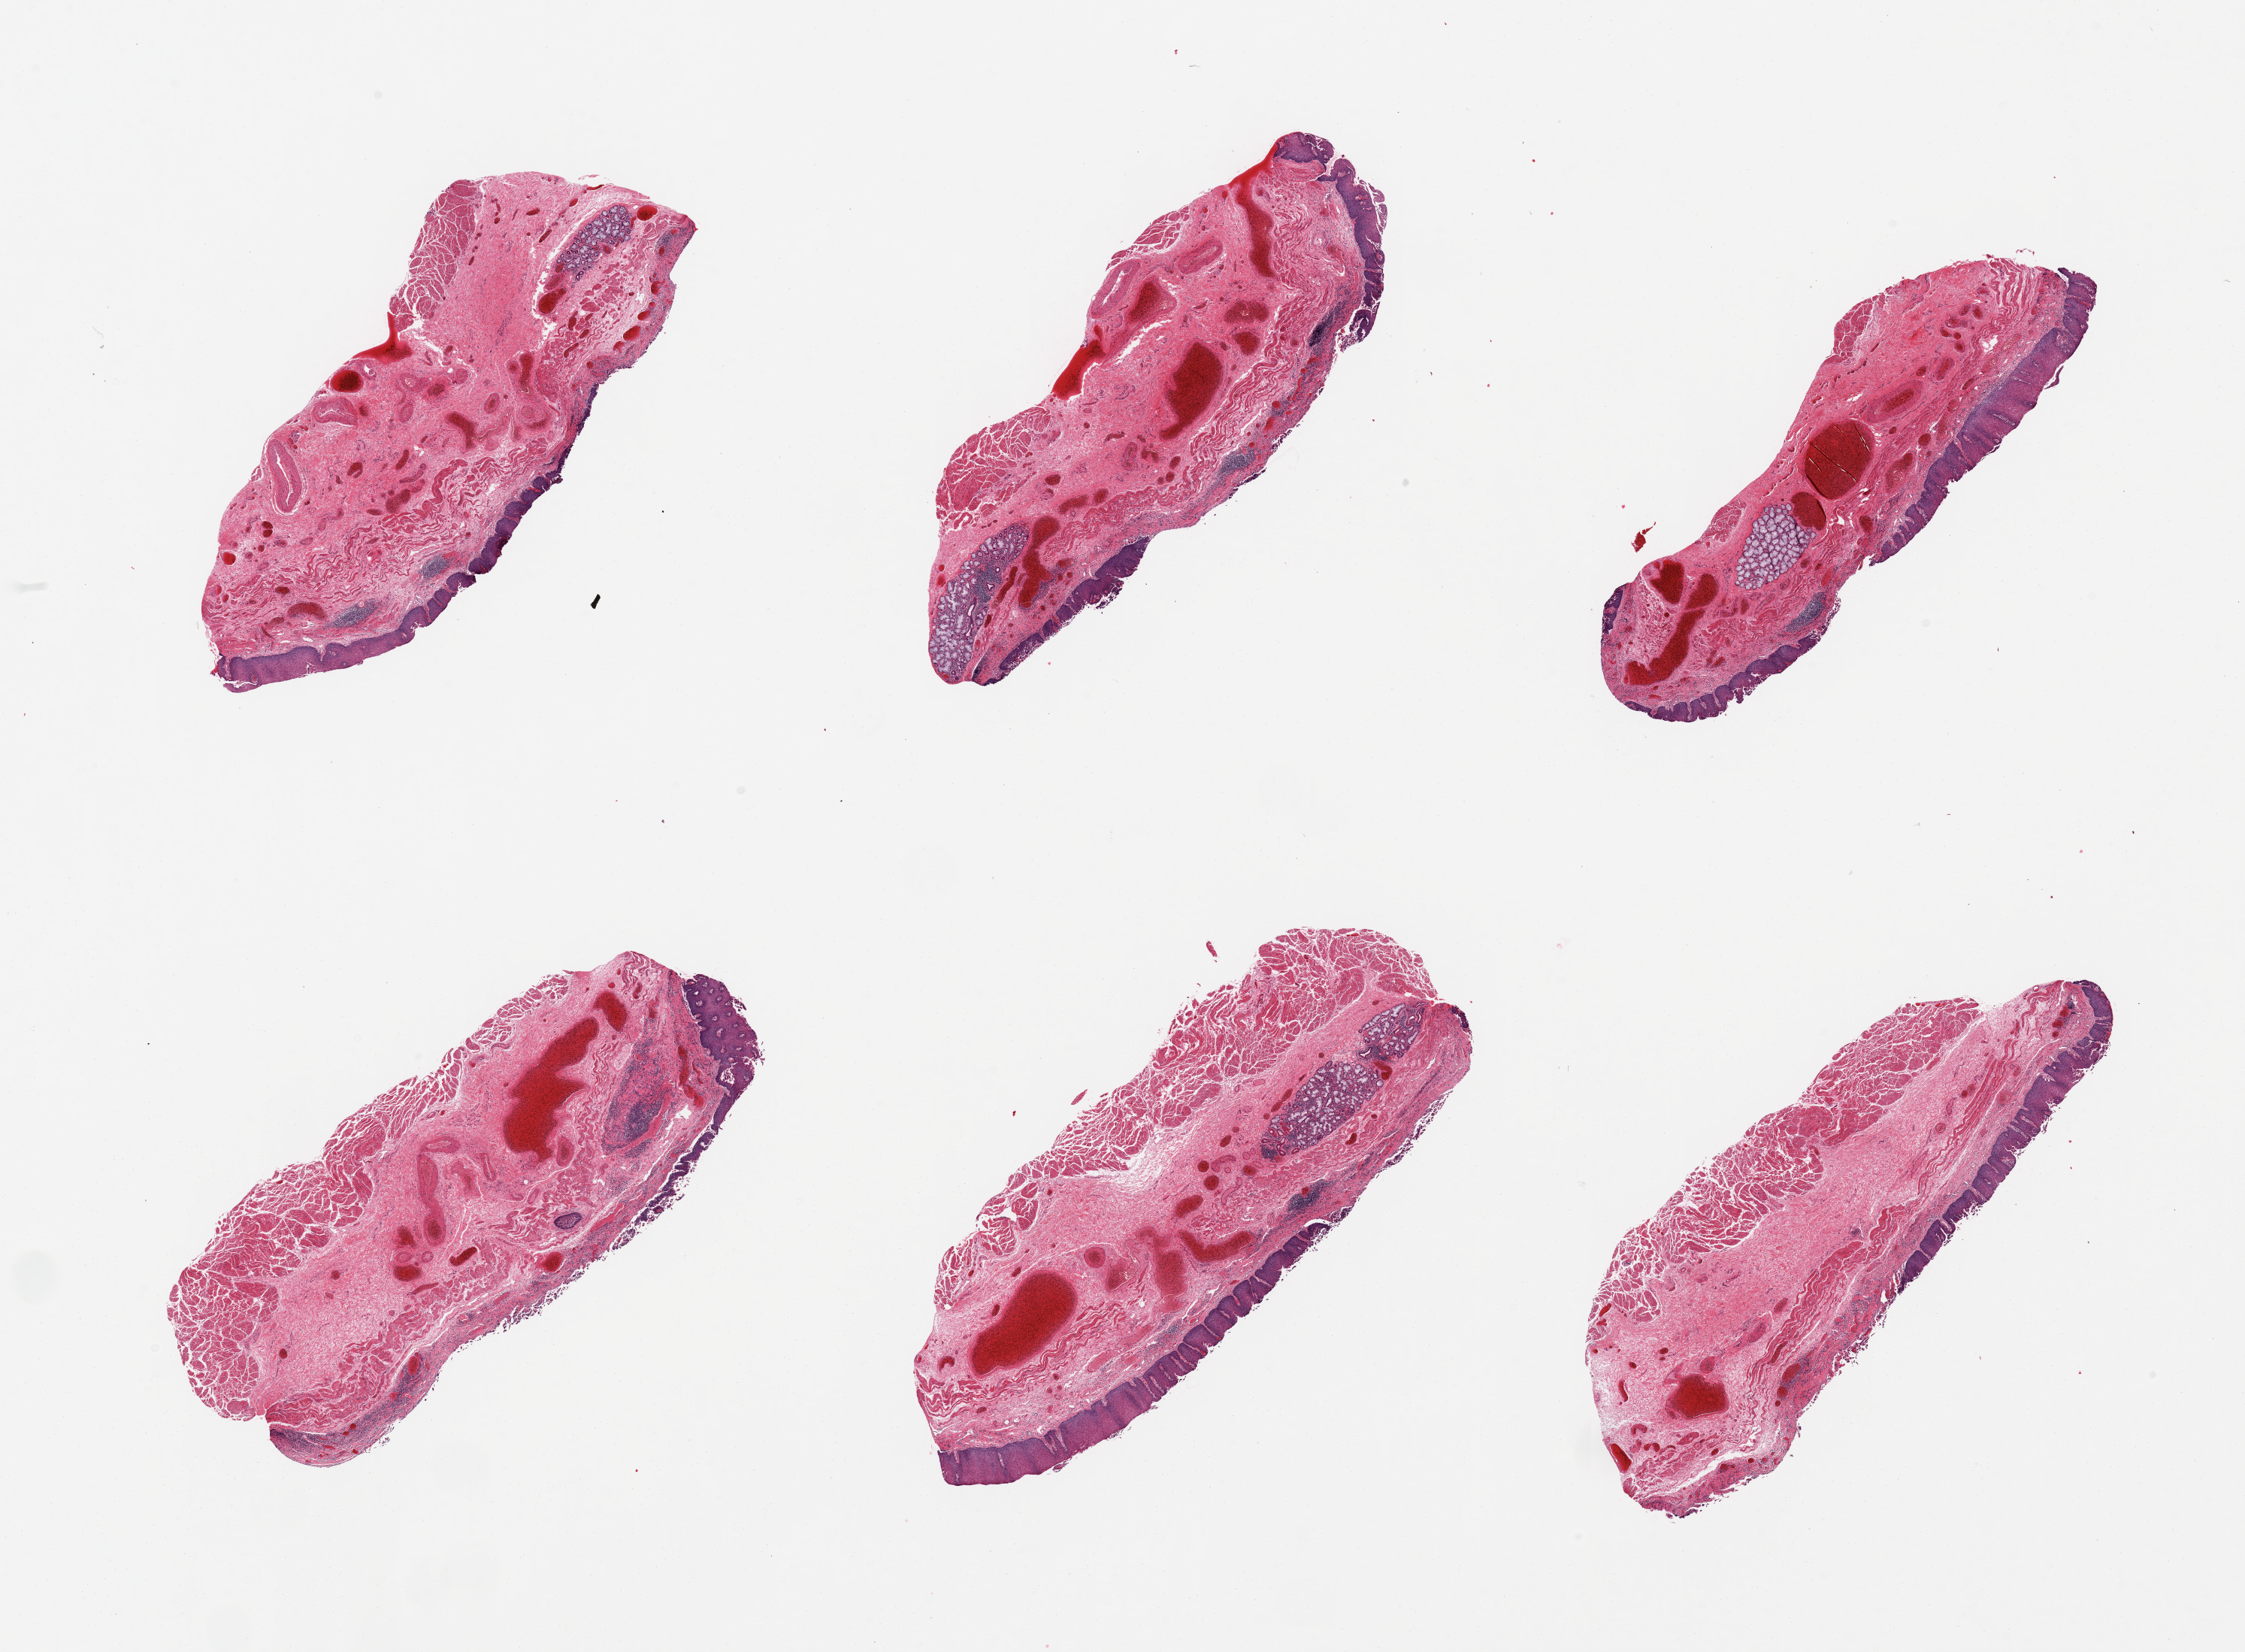
Digitized H&E-stained section, shown as a low-resolution overview of the whole scanned area (about 23.6 x 17.4 mm); PAXgene-fixed, paraffin-embedded tissue; section of esophageal mucous membrane (target tissue); tissue donor sample. Male donor.
Review note (as recorded): 6 pieces; squamous mucosa is partially sloughed, congestion and chronic inflammation, all pieces include muscularis propria (not target).